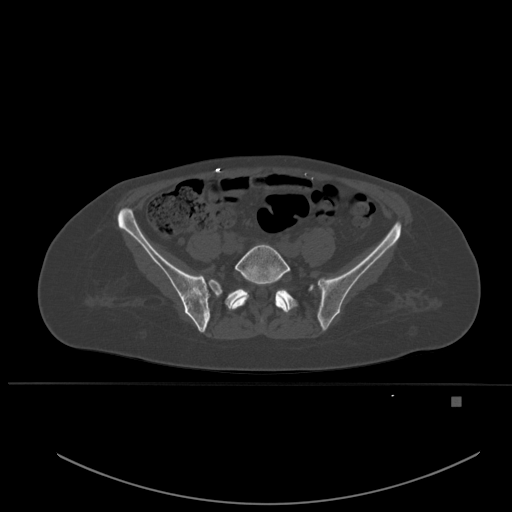
CT including the spine, one axial slice; slice 148 of 651 in the series (ordered by position); bone window (W 1800 / L 400 HU); 512 × 512 image matrix. Patient: female, 49 years. From the clinical record (not read from this slice): primary cancer: breast.
Outlined on this slice (semi-automatic segmentation, software-assisted and operator-edited):
- L5 vertebra: bounding box (x1, y1, x2, y2) in pixels: (230, 244, 291, 322)